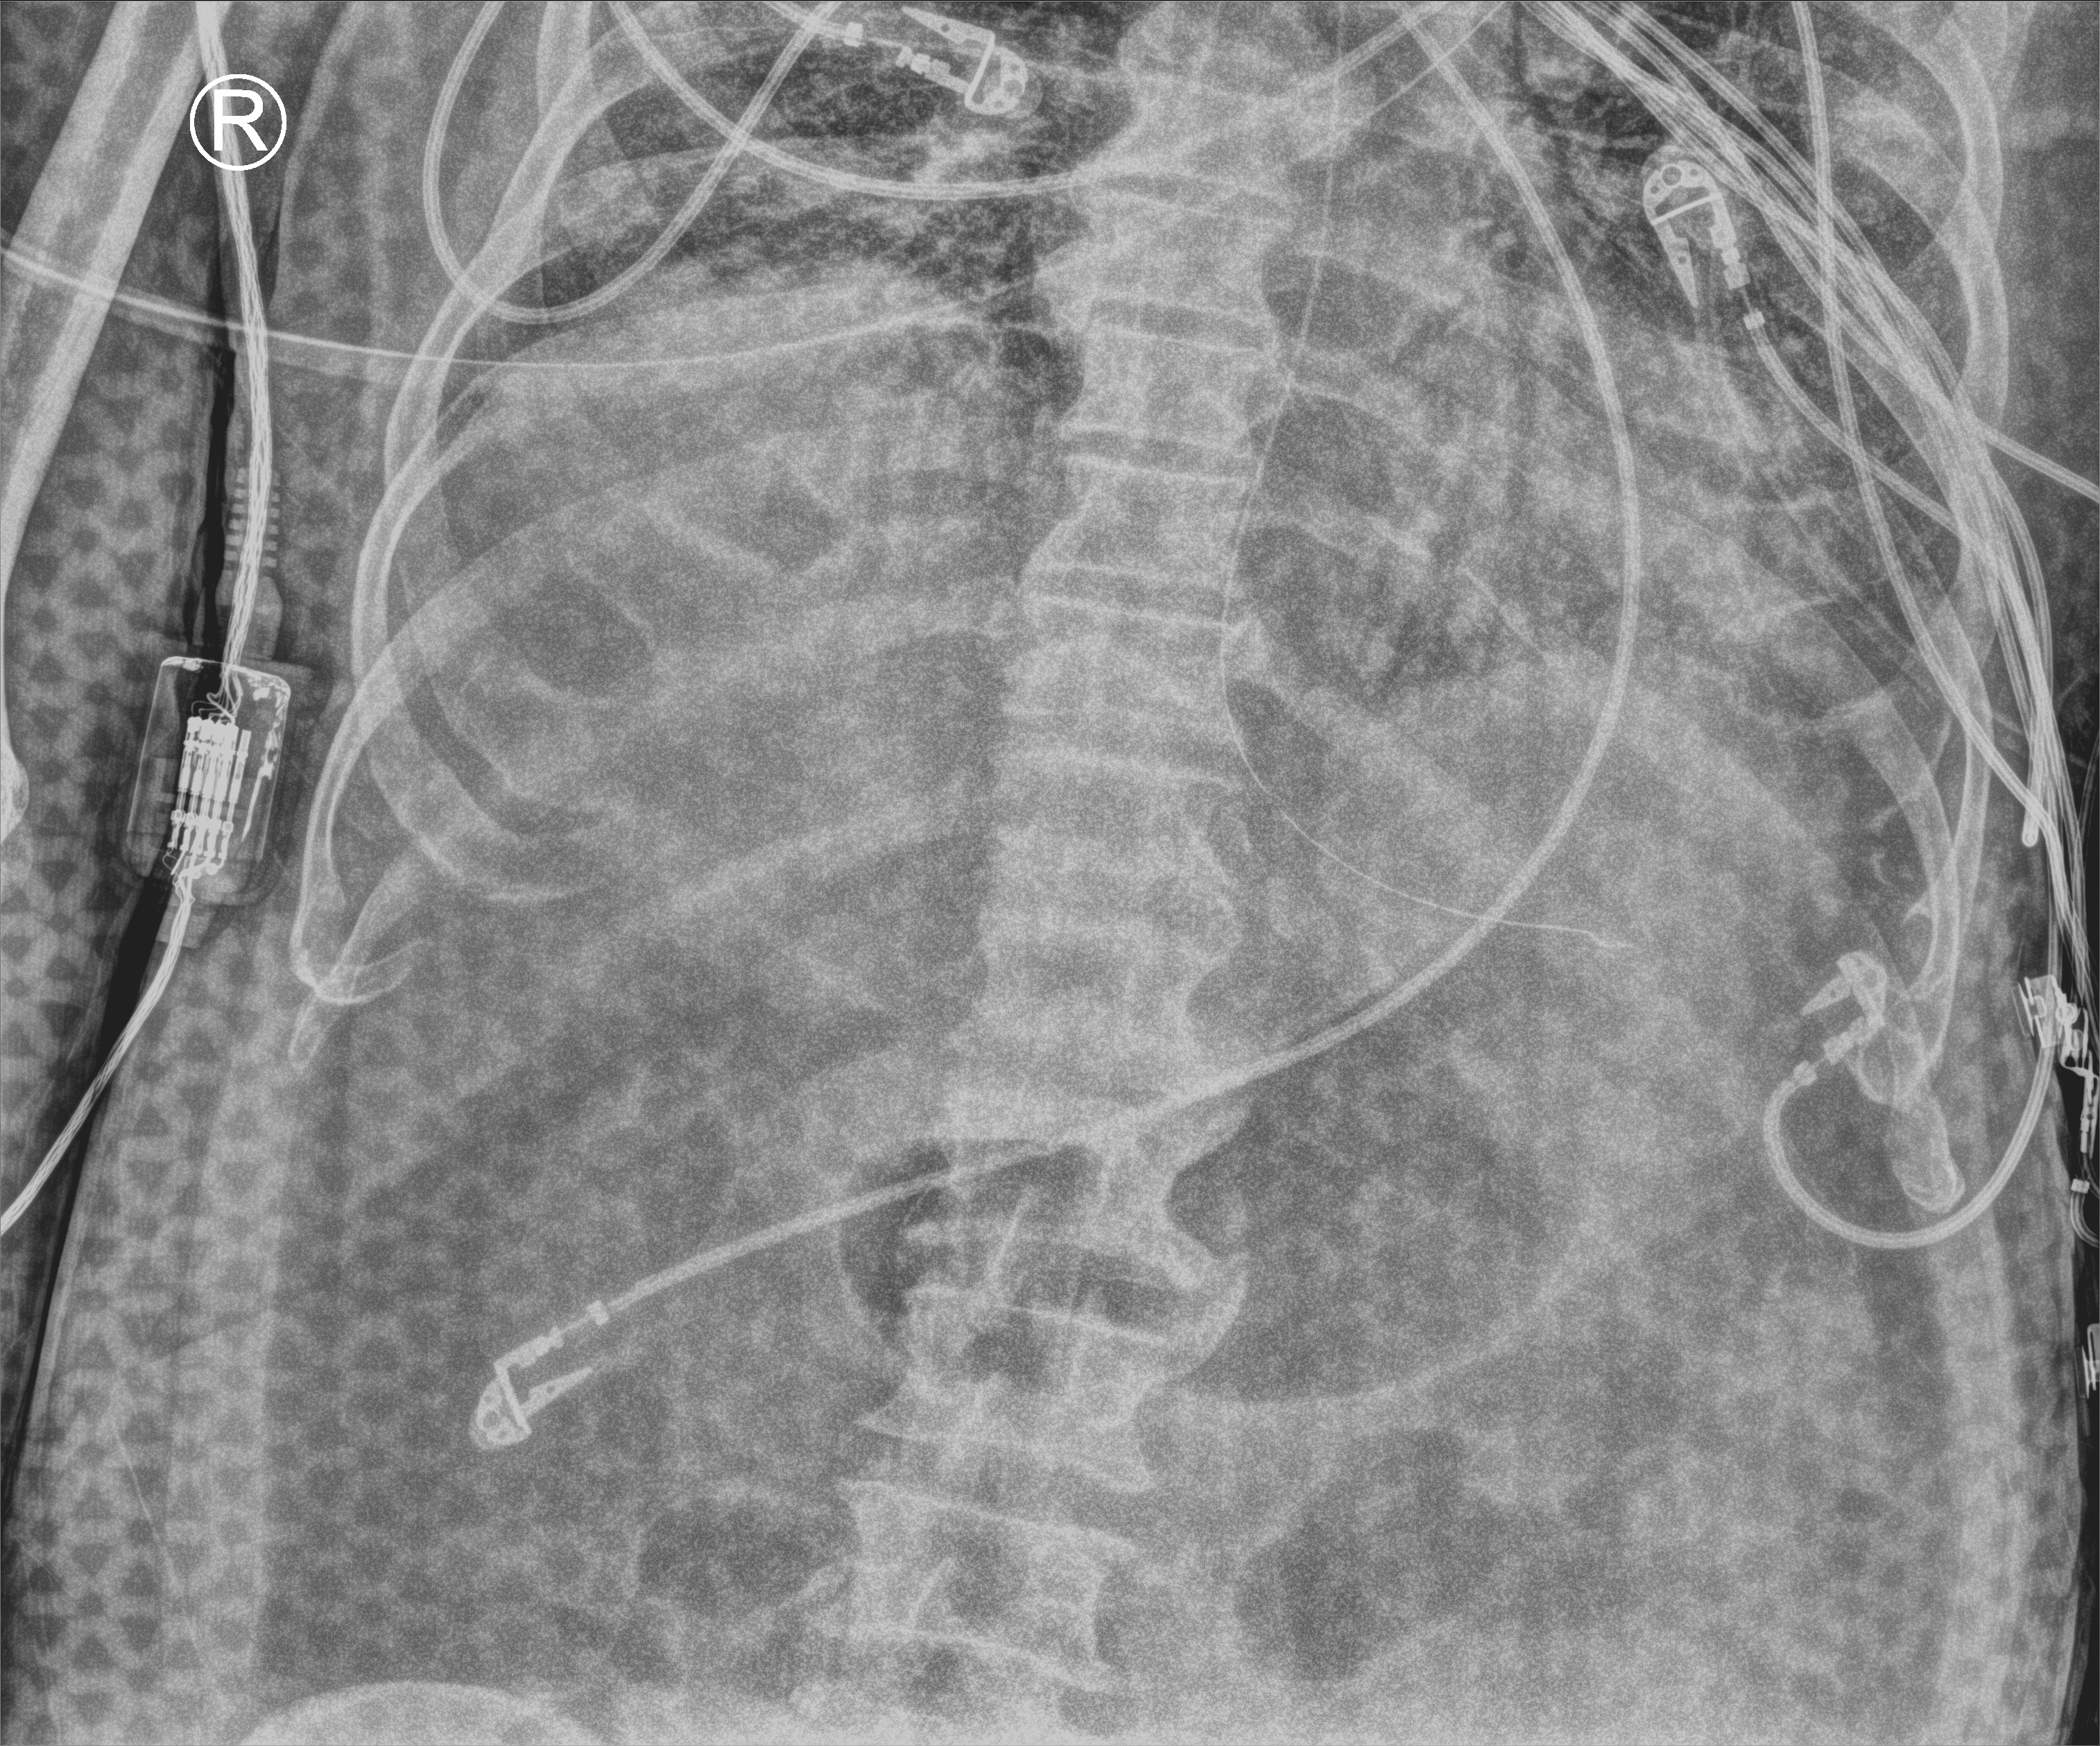
Portable chest radiograph, anteroposterior (AP) projection. Male patient hospitalised with COVID-19, age 75–90 years.
Admission-level facts for this patient (not findings on this image; timing relative to this image not recorded): hypertension (admission record): yes; admitted to intensive care during this hospital stay: yes; length of hospital stay: 33 days.